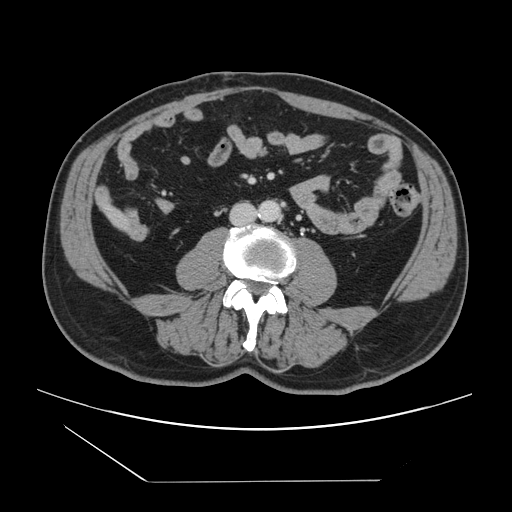
Contrast-enhanced abdominal CT, one axial slice. Position 11 of 157 along the scan axis. 120 kVp. Soft-tissue window (W 400 / L 40 HU). 2.5 mm slice thickness. 512 × 512 image matrix, field of view 407 × 407 mm. Male patient, age 61 years. Case-level facts recorded for this patient, not image findings: diagnosis: colorectal cancer liver metastases, imaged before liver resection; multiple liver metastases: yes; largest metastasis: 5.5 cm; disease in both lobes: yes.
Structures marked on this image (outlined manually by an expert reader):
- liver: bounding box <106,207,124,228> (left, top, right, bottom; pixels)
- planned liver remnant (the part of the liver to remain after resection): <105,206,117,216>